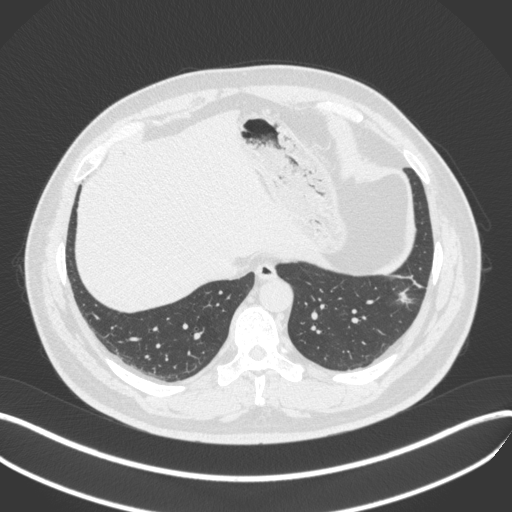
Chest CT, one axial slice. Position 106 of 420 along the scan axis. Reconstruction kernel B31f. 120 kVp. Lung window (W 1500 / L -600 HU). 1 mm slice thickness. 512 × 512 image matrix, field of view 400 × 400 mm. Patient: male, 39 years. From the clinical record (not read from this slice): clinical TNM (as recorded): T2a N0 M0.
Structures marked on this image (rectangle marked by the reading radiologist):
- lung tumour (recorded histology: adenocarcinoma): box from (x=394, y=282) to (x=416, y=310) px